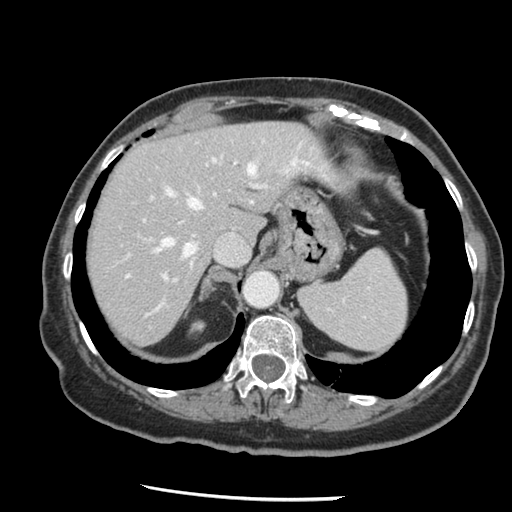
Contrast-enhanced abdominal CT, one axial slice. Slice 103 of 148 in the series (ordered by position). 120 kVp. Intravenous contrast given. Soft-tissue window (W 400 / L 40 HU). 2.5 mm slice thickness. 512 × 512 image matrix, field of view 330 × 330 mm. Female patient, age 85 years. Case-level facts recorded for this patient, not image findings: diagnosis: colorectal cancer liver metastases, imaged before liver resection; multiple liver metastases: no; largest metastasis: 0.9 cm; chemotherapy before resection: yes.
Annotated regions visible in this slice (outlined manually by an expert reader):
- hepatic veins: box from (x=127, y=138) to (x=295, y=277) px
- liver: (x=87, y=122)–(x=329, y=345)
- planned liver remnant (the part of the liver to remain after resection): (x=87, y=122)–(x=329, y=345)
- portal vein (with intrahepatic branches): (x=143, y=156)–(x=265, y=310)